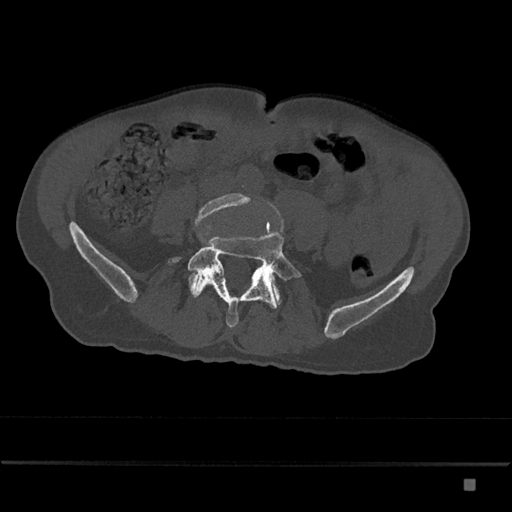
CT including the spine, one axial slice; position 288 of 797 along the scan axis; 120 kVp; bone window (W 1800 / L 400 HU); 0.5 mm slice thickness; 512 × 512 image matrix, field of view 390 × 390 mm. Patient: male, 72 years. Case-level facts recorded for this patient, not image findings: primary cancer: prostate.
Outlined on this slice (semi-automatic segmentation, software-assisted and operator-edited):
- L4 vertebra: bounding box (x1, y1, x2, y2) in pixels: (194, 193, 254, 227)
- L5 vertebra: (167, 232, 302, 328)